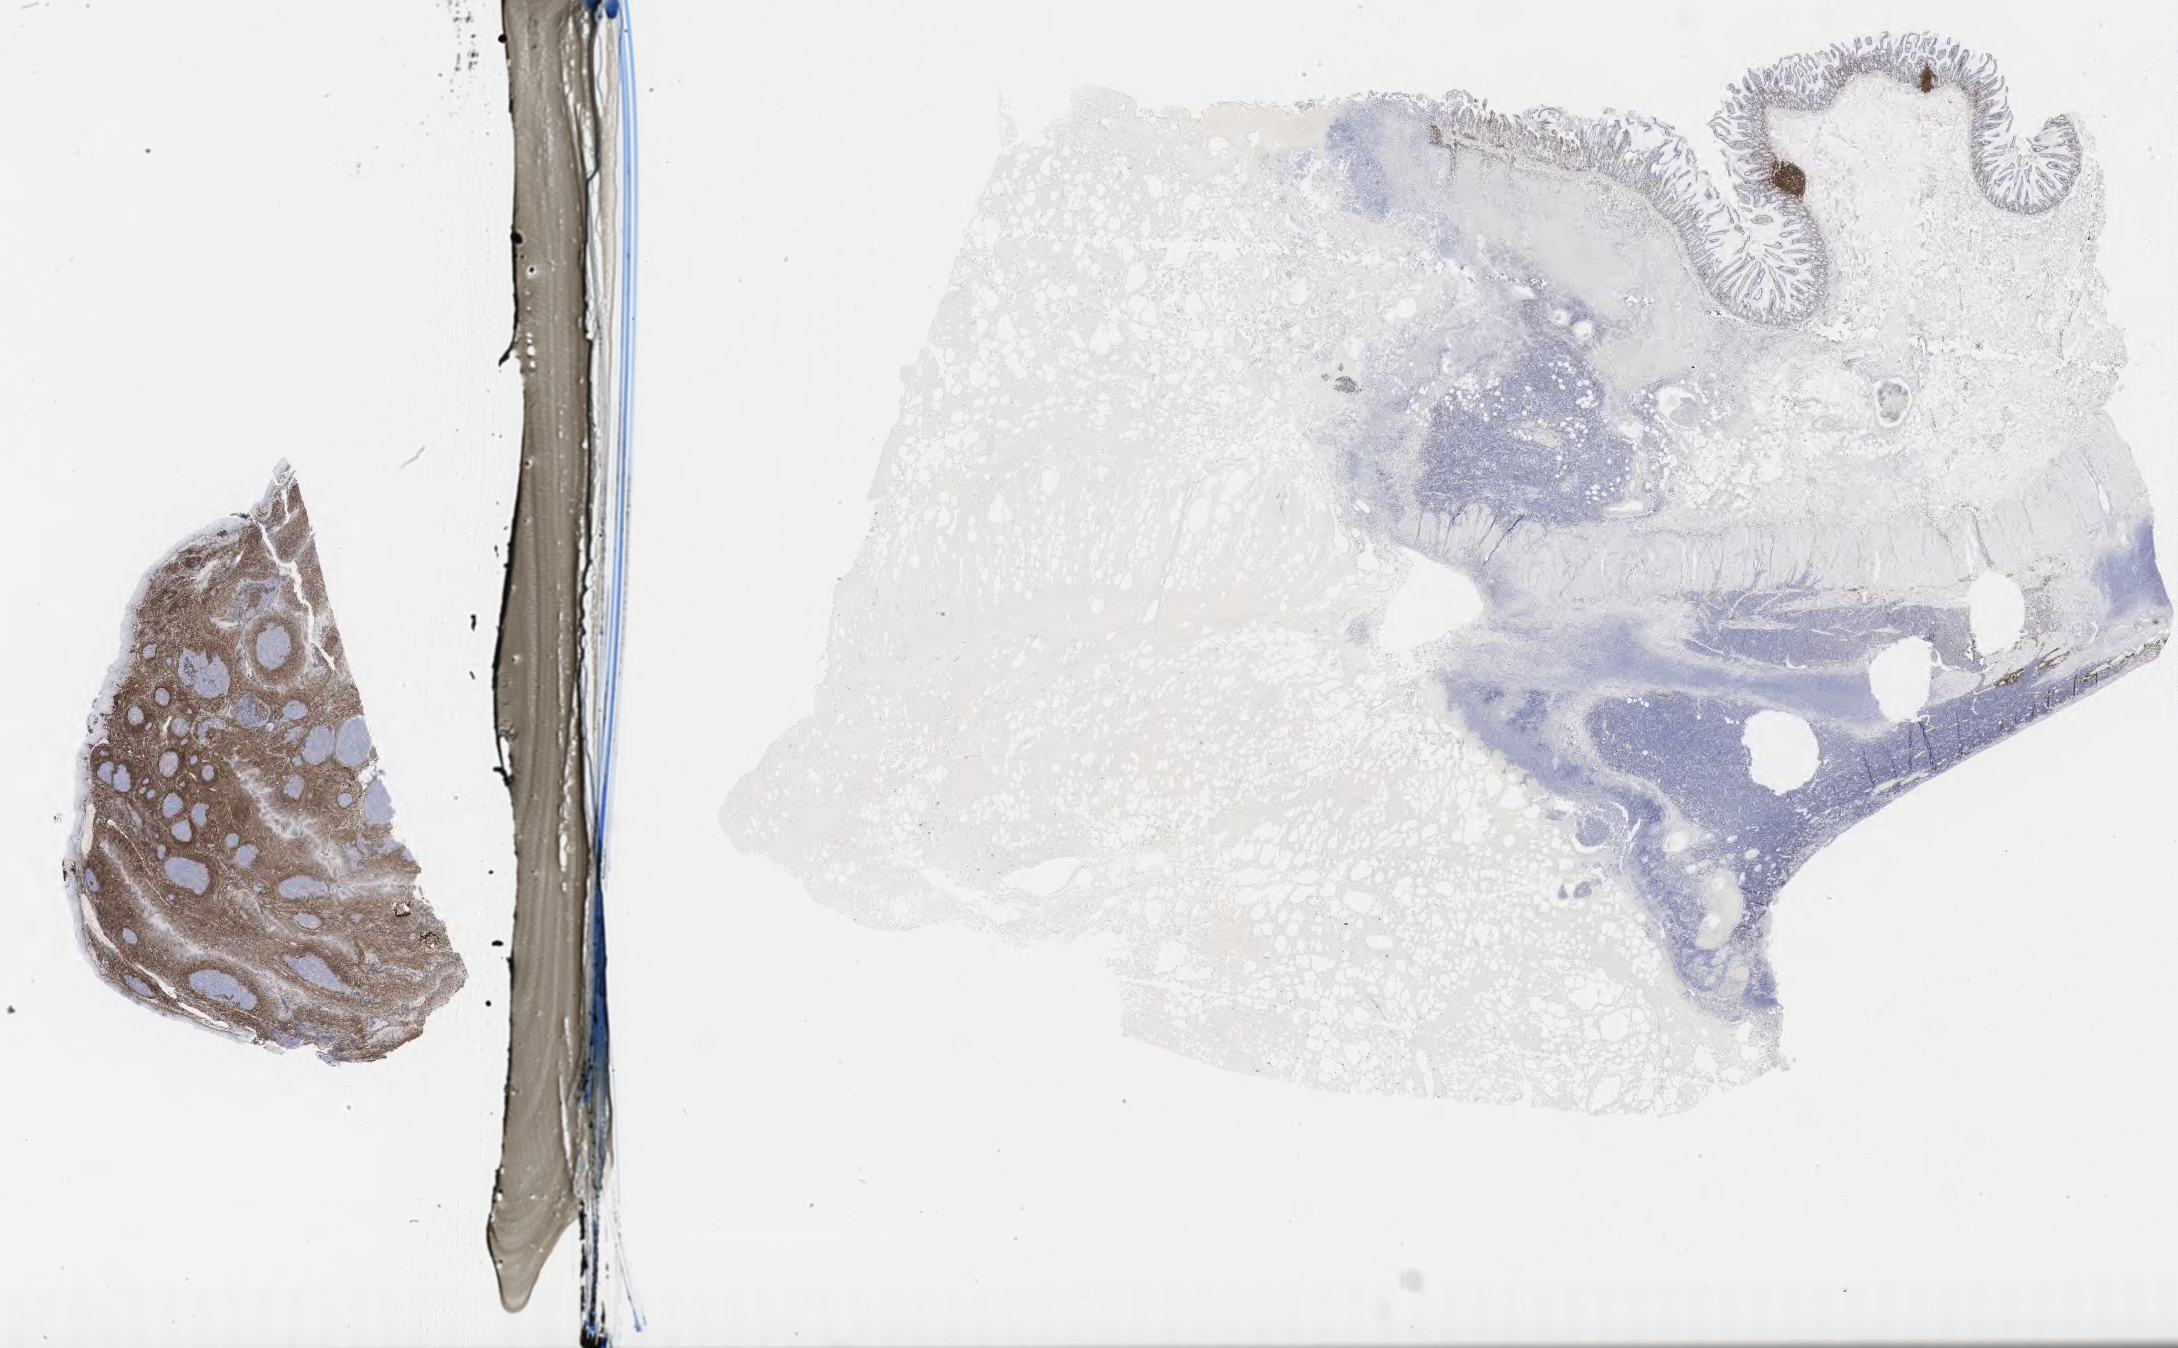
Immunohistochemistry (IHC) whole-slide image stained for BCL2 — shown as a low-resolution overview of the whole scanned area (about 35.2 x 21.8 mm), tumor tissue, anatomic site: colon. Male patient, 62 years old.
* histologic diagnosis: Burkitt lymphoma, NOS